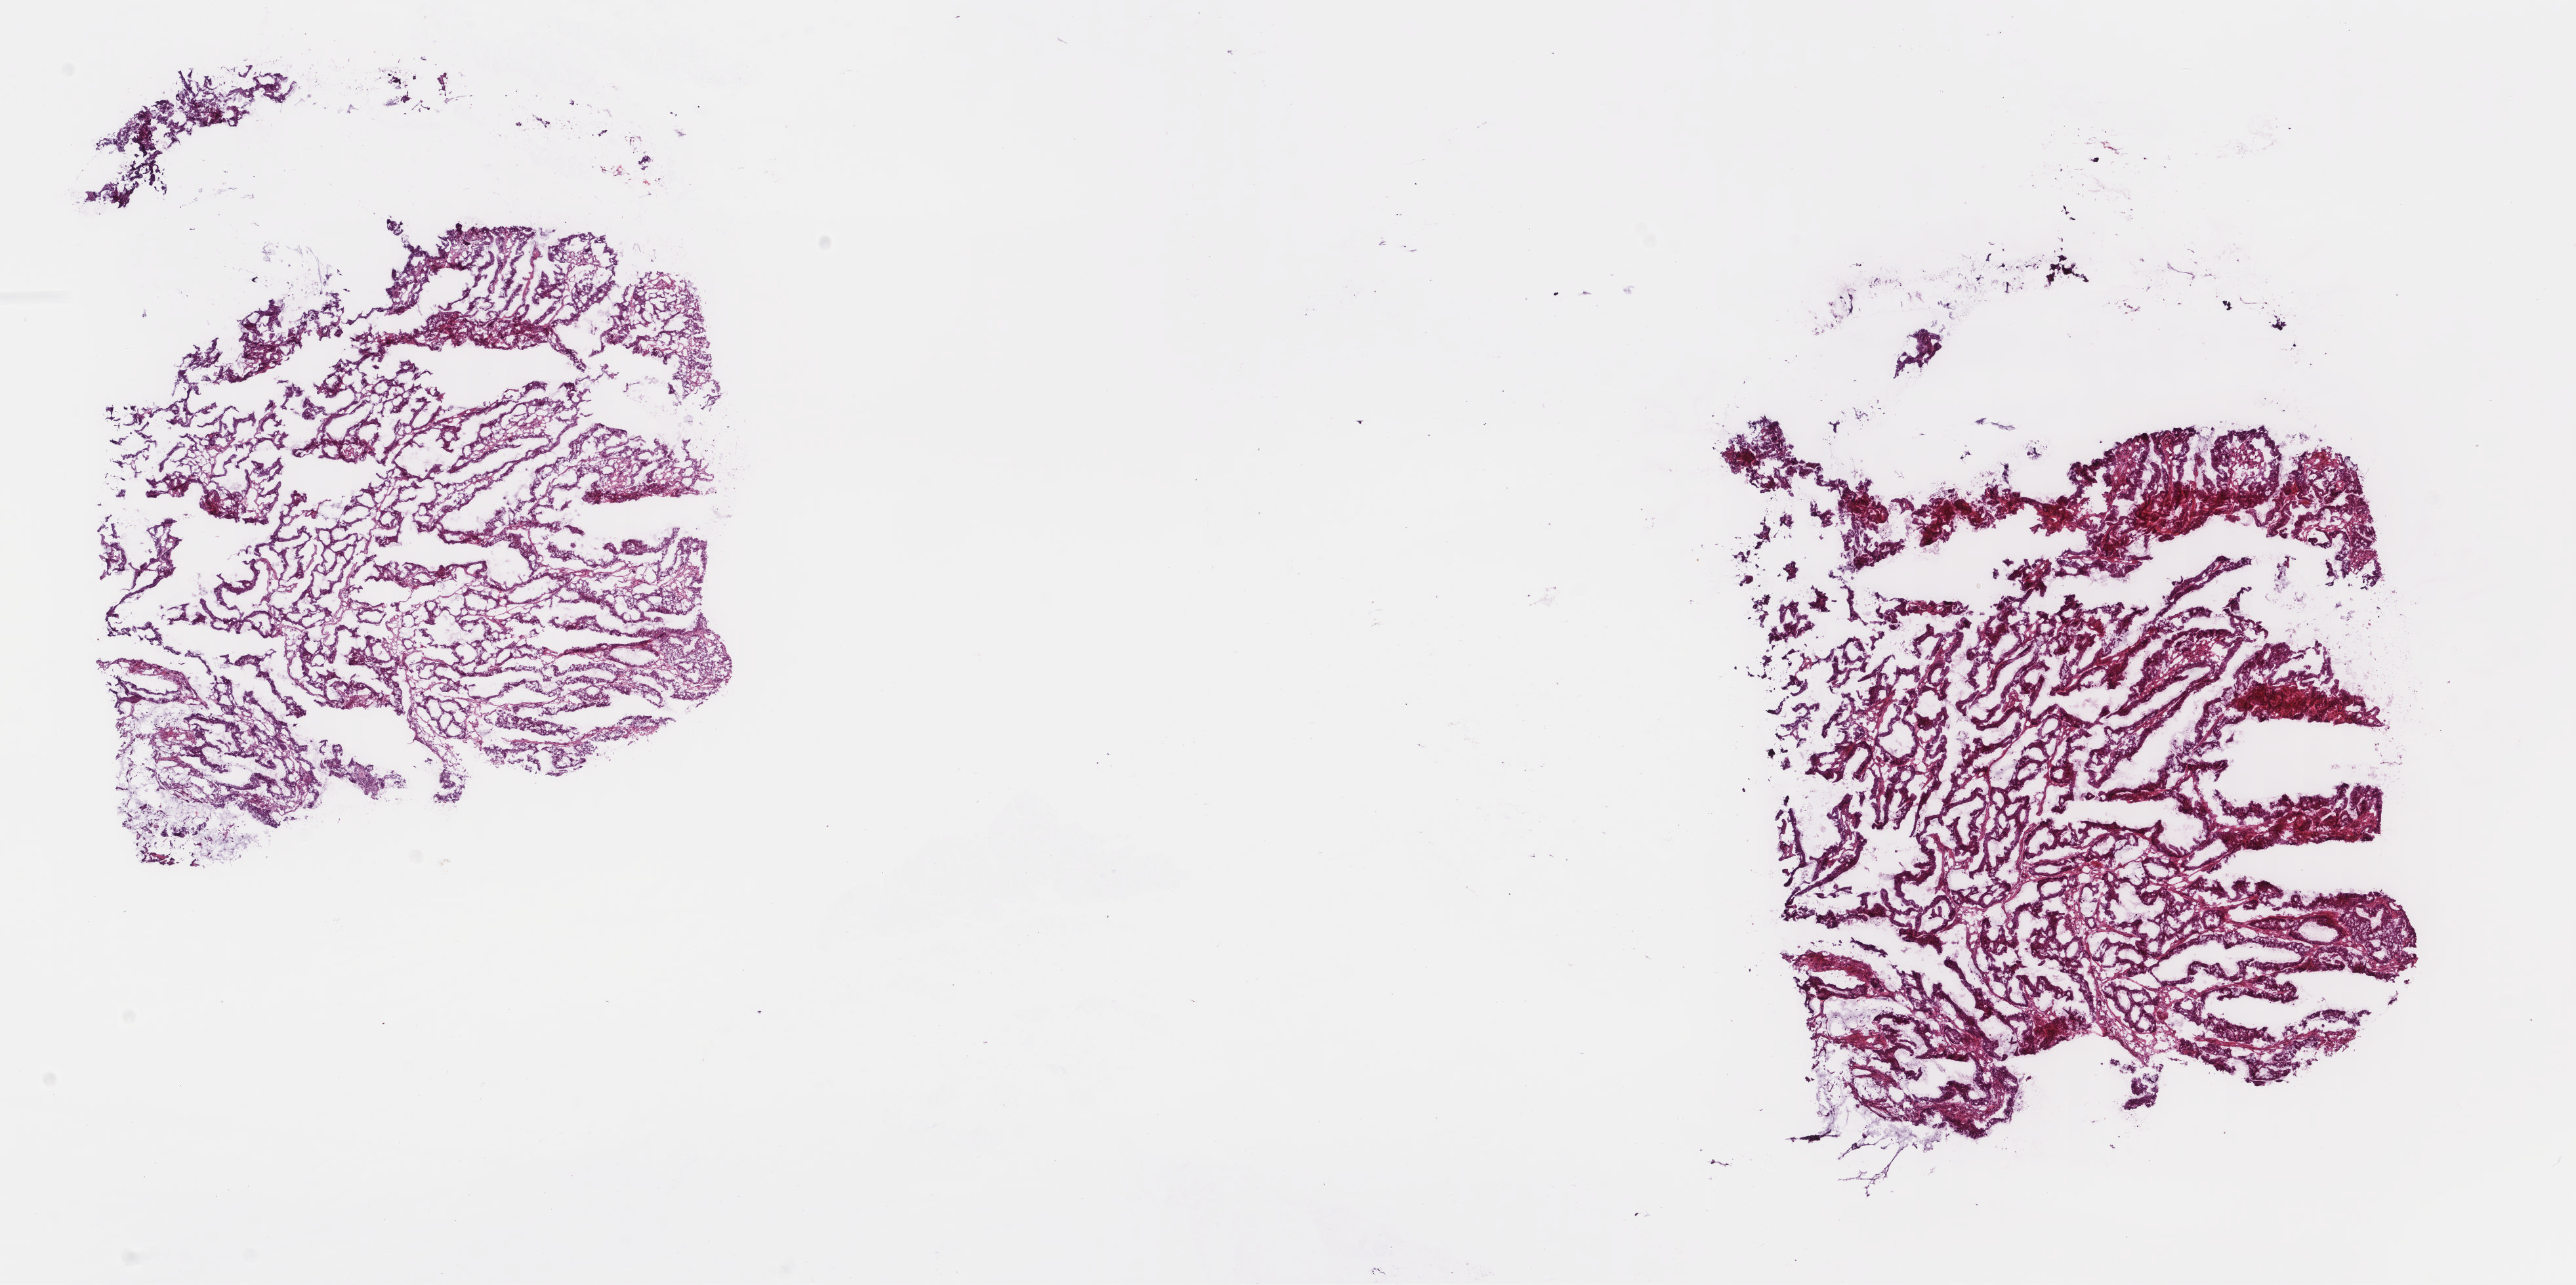
Whole-slide histology image, H&E — low-resolution overview of the scanned area, about 15.6 x 7.8 mm; frozen section from the top of the tissue portion; colon, primary tumour sample. Patient: male, age at initial diagnosis 75 years. Slide review estimates, as recorded: tumour cells 75%, tumour nuclei 75%, normal cells 0%, stromal cells 22%, necrosis 3%. Inflammatory infiltration, as recorded: lymphocyte infiltration 10%, monocyte infiltration 0%, neutrophil infiltration 0%.
Diagnosis: Mucinous adenocarcinoma. Lymph nodes positive (case pathology): 0 of 17 examined. AJCC pathologic stage: IIA (6th edition).